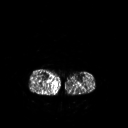
FDG PET of an extremity soft-tissue mass (from a PET/CT study), one axial slice. Position 121 of 267 along the scan axis. 3.27 mm slice thickness. 128 × 128 image matrix, field of view 500 × 500 mm. Male patient, age 69 years. From the clinical record (not read from this slice): histological type: pleiomorphic liposarcoma; grade: high; site of the primary tumour: right calf.
Outlined on this slice (expert contour drawn on MRI and transferred to this co-registered scan by the dataset authors):
- gross tumour volume including surrounding oedema: bounding box (x1, y1, x2, y2) in pixels: (52, 83, 56, 87)